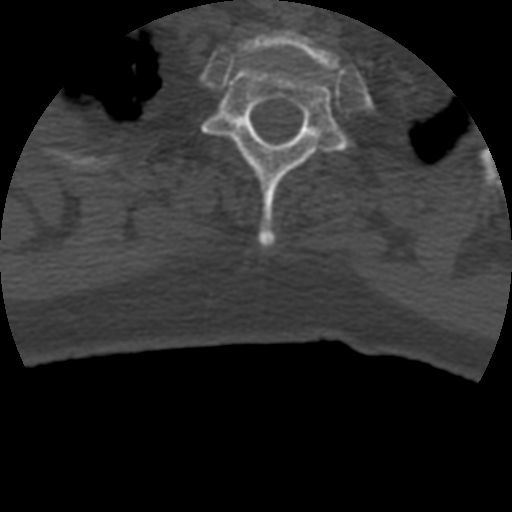
CT including the spine, one axial slice; slice 369 of 399 in the series (ordered by position); 120 kVp; bone window (W 1800 / L 400 HU); 1.25 mm slice thickness; 512 × 512 image matrix. Patient age 69 years. Case-level facts recorded for this patient, not image findings: primary cancer: prostate.
Outlined on this slice (semi-automatic segmentation, software-assisted and operator-edited):
- T1 vertebra: bounding box [x1, y1, x2, y2] px = [242, 30, 339, 70]
- T2 vertebra: [202, 60, 347, 249]